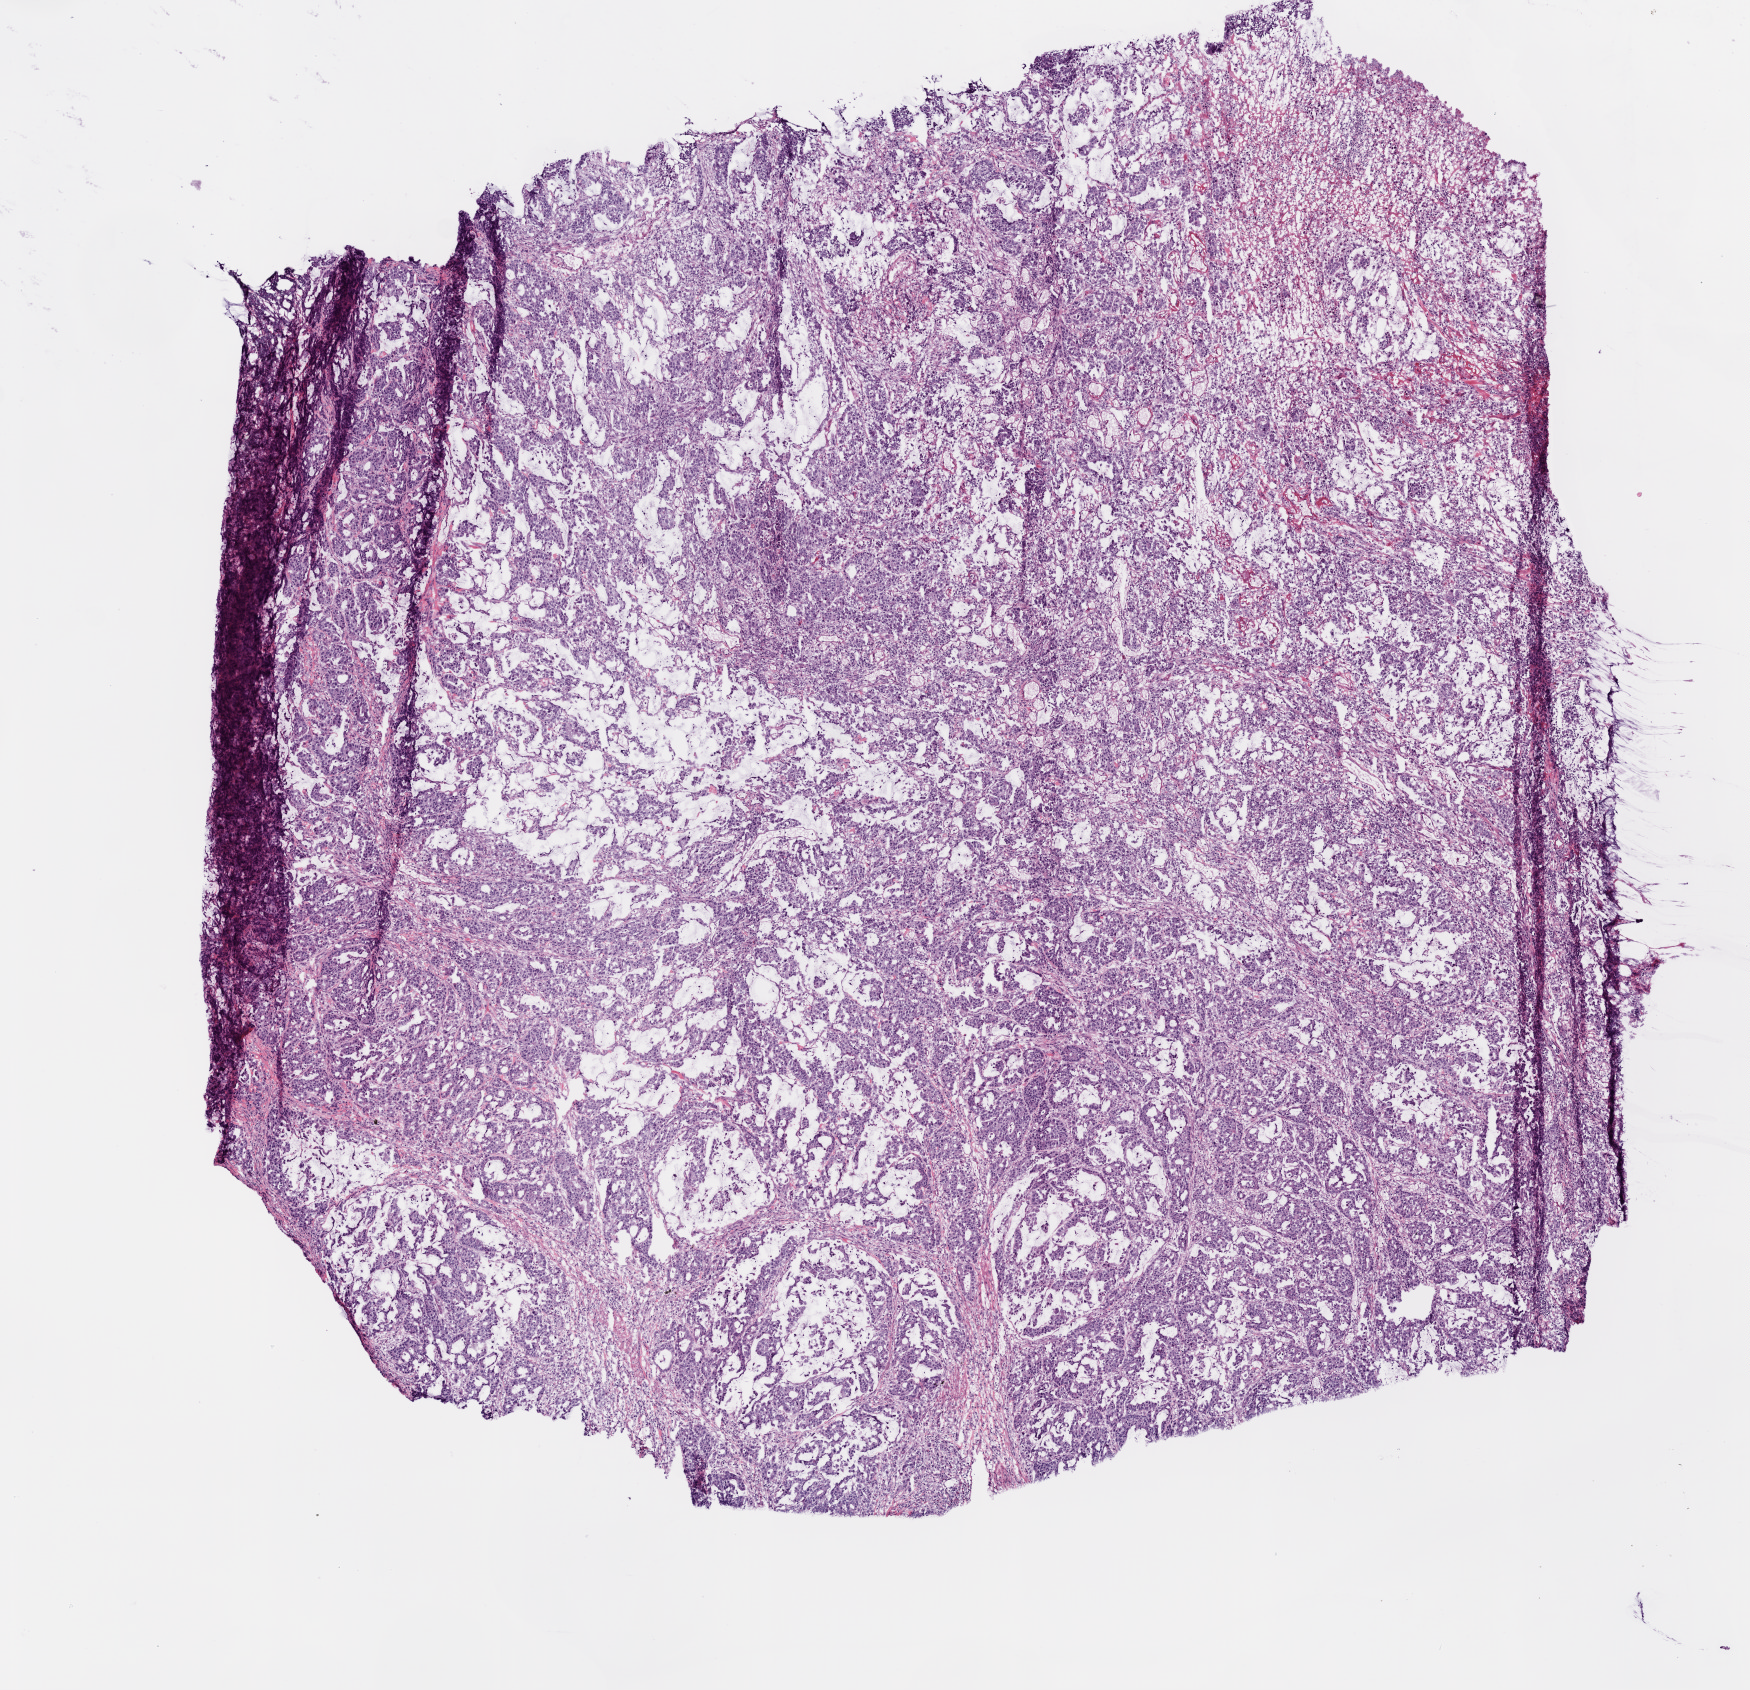
Hematoxylin and eosin (H&E) stained whole-slide image — shown as a low-resolution overview of the whole scanned area (about 7.0 x 6.8 mm, slide scanned at 20x), frozen section from the bottom of the tissue portion, sample: primary tumour, colon. Patient: female, age at initial diagnosis 89 years. Composition of this section per pathologist review: tumour cells 95%, tumour nuclei 90%, normal cells 0%, stromal cells 0%, necrosis 5%.
* AJCC pathologic stage: IIA (6th edition)
* diagnosis: Mucinous adenocarcinoma
* lymph nodes positive (case pathology): 0 of 14 examined